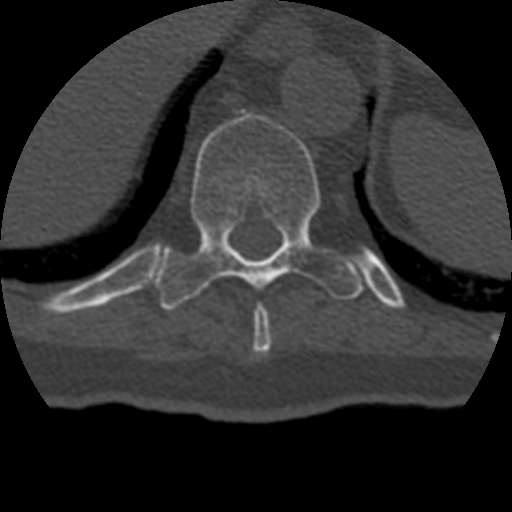
CT including the spine, one axial slice; position 221 of 399 along the scan axis; reconstruction kernel STANDARD; bone window (W 1800 / L 400 HU); 512 × 512 image matrix, field of view 160 × 160 mm. Patient age 69 years. Case-level facts recorded for this patient, not image findings: primary cancer: prostate.
Outlined on this slice (semi-automatically segmented with operator editing):
- T10 vertebra: bounding box (x1, y1, x2, y2) in pixels: (157, 114, 363, 310)
- T9 vertebra: (253, 305, 272, 356)